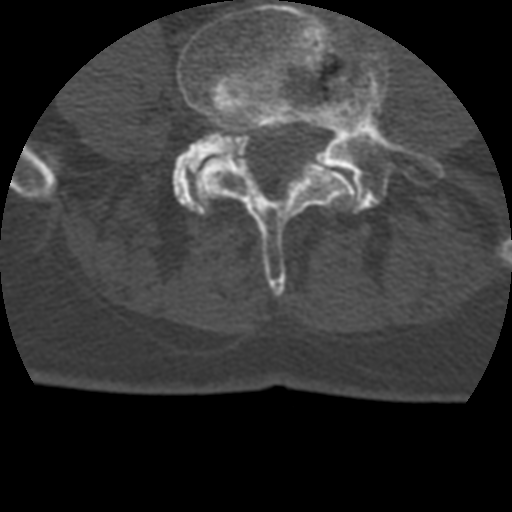
CT including the spine, one axial slice. Slice 56 of 399 in the series (ordered by position). 120 kVp. Bone window (W 1800 / L 400 HU). 512 × 512 image matrix, field of view 160 × 160 mm. Patient age 69 years. Case-level facts recorded for this patient, not image findings: primary cancer: prostate.
Annotated regions visible in this slice (semi-automatic segmentation, software-assisted and operator-edited):
- L4 vertebra: bounding box (x1, y1, x2, y2) in pixels: (177, 0, 355, 297)
- L5 vertebra: (172, 50, 432, 210)